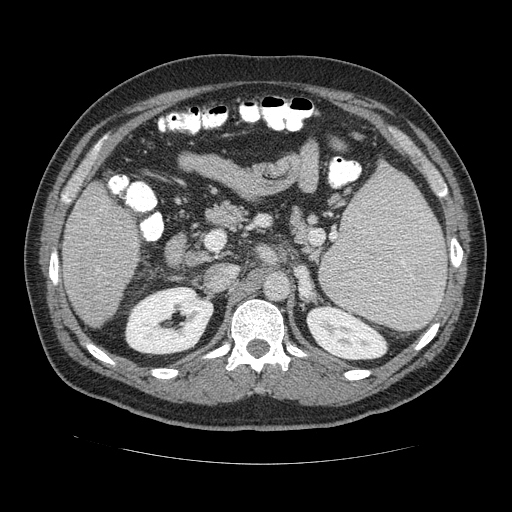
Contrast-enhanced abdominal CT (liver protocol), one axial slice; position 65 of 113 along the scan axis; reconstruction kernel STANDARD; 120 kVp; soft-tissue window (W 400 / L 40 HU); 2.5 mm slice thickness; 512 × 512 image matrix, field of view 400 × 400 mm. Case-level facts recorded for this patient, not image findings: diagnosis: hepatocellular carcinoma (patient treated with transarterial chemoembolisation; whether this scan precedes or follows treatment is not stated here); TNM stage (as recorded): Stage-II; Child-Pugh class: B; tumour differentiation: moderately differentiated; tumour nodularity: multinodular.
Structures marked on this image (semi-automatic segmentation, software-assisted and operator-edited):
- liver parenchyma outside the tumour (the mass and vessels are separate outlines, so this box may not span the whole liver): bounding box <60,180,144,328> (left, top, right, bottom; pixels)
- liver vessels: <92,212,102,276>